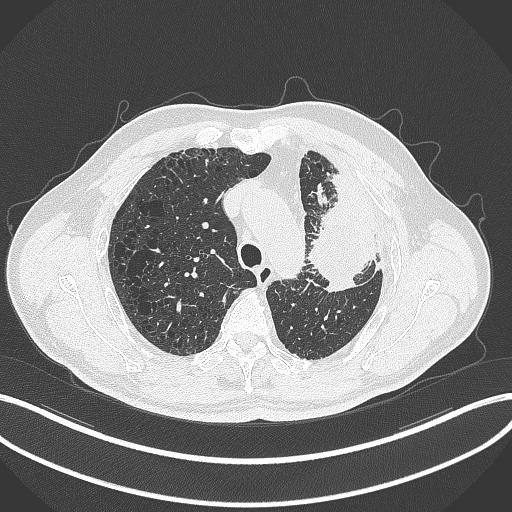
Chest CT, one axial slice. Slice 237 of 297 in the series (ordered by position). Lung window (W 1500 / L -600 HU). 1 mm slice thickness. 512 × 512 image matrix. Patient: male, 68 years. Case-level facts recorded for this patient, not image findings: clinical TNM (as recorded): T3 N3 M1.
Outlined on this slice (bounding box drawn by a radiologist):
- lung tumour (recorded histology: adenocarcinoma): bounding box <303,175,382,293> (left, top, right, bottom; pixels)